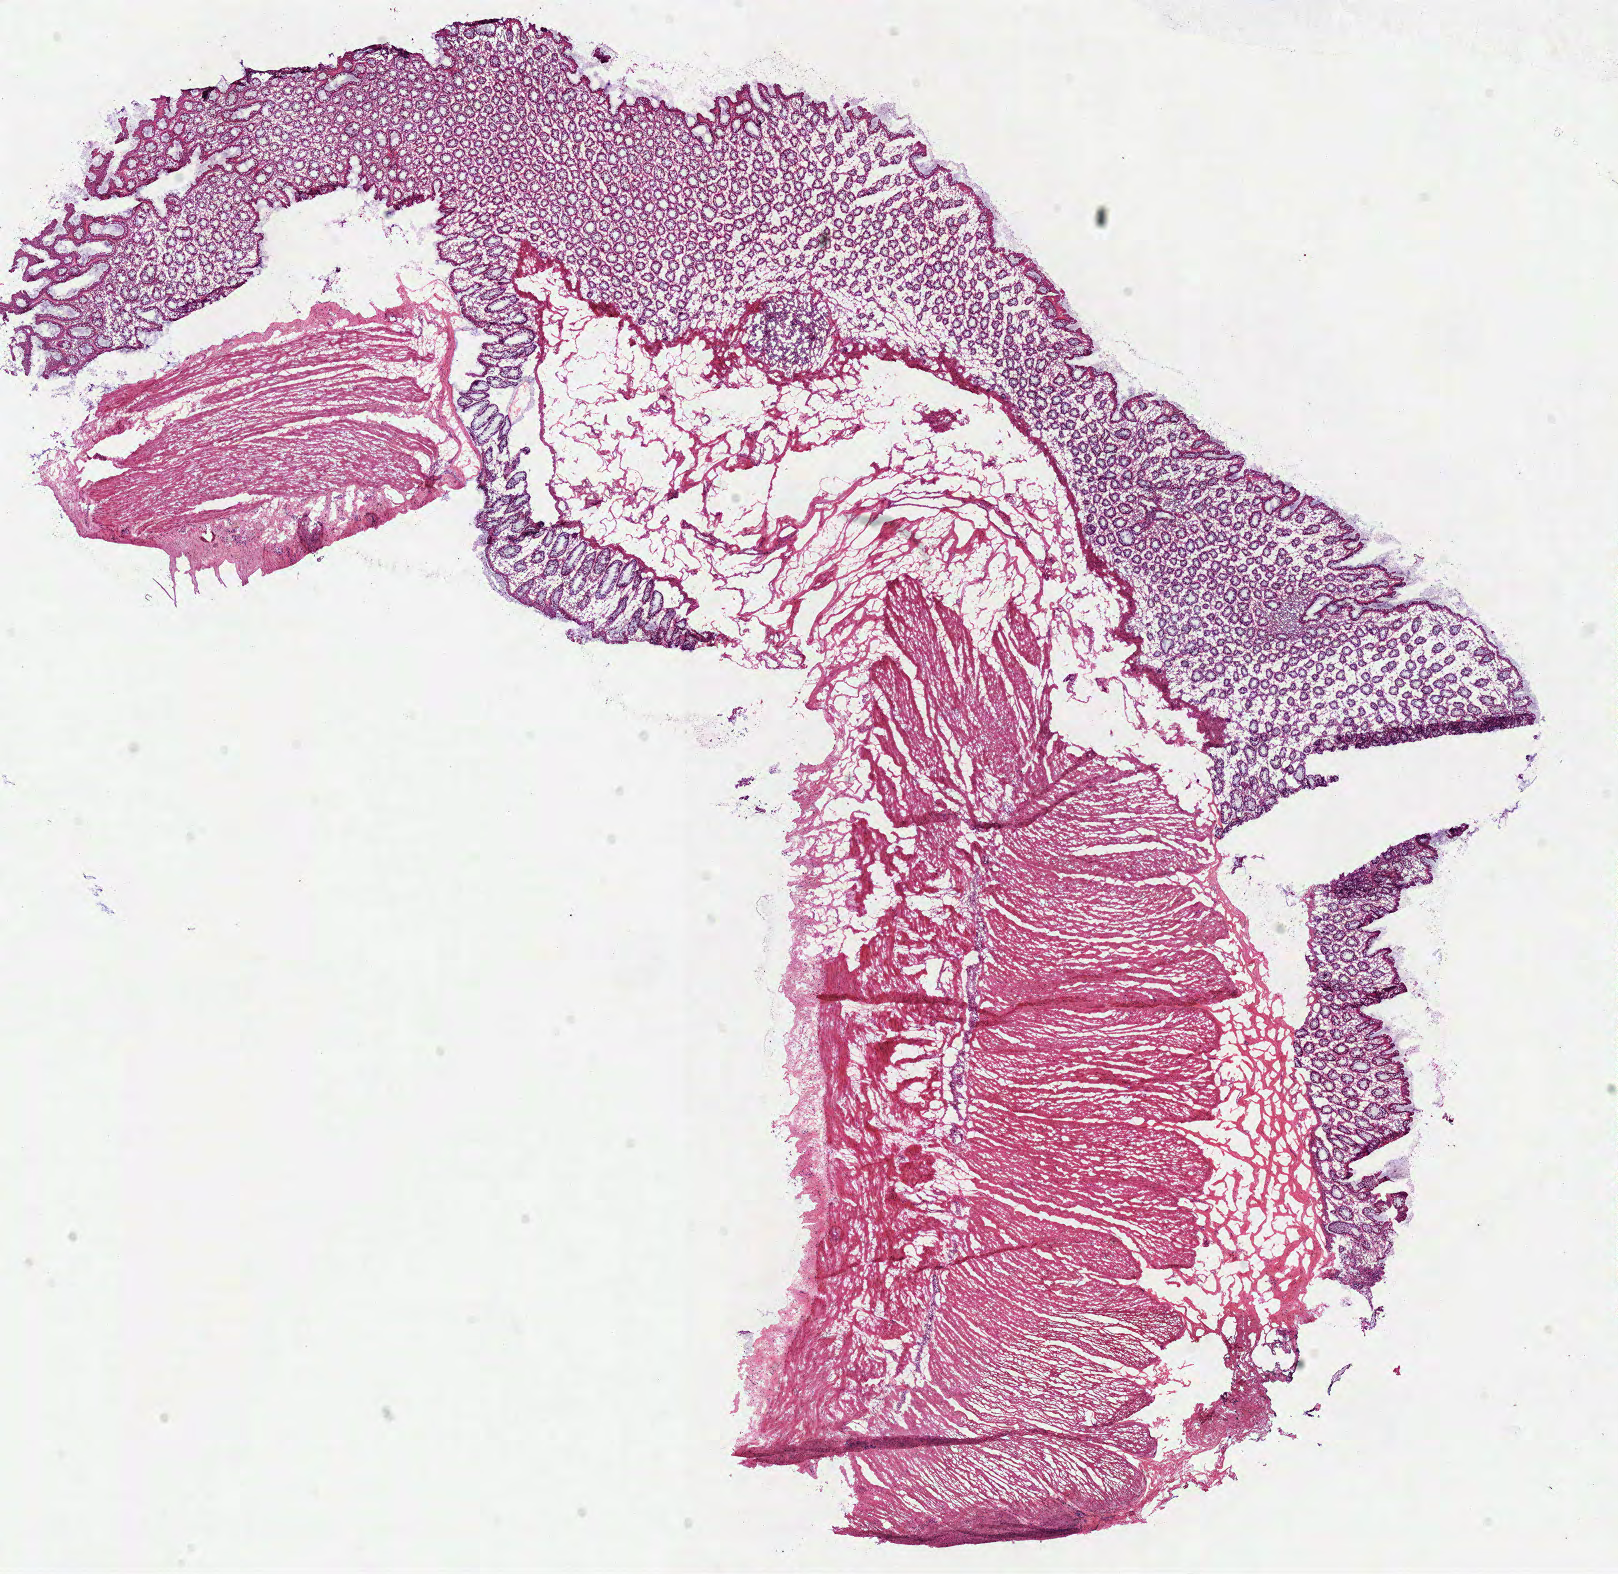
H&E-stained whole-slide image — low-resolution overview of the scanned area, about 12.7 x 12.4 mm (from a 40x scan), frozen section from the top of the tissue portion, sample: solid tissue normal (non-tumour tissue), colon. Female patient; age at initial diagnosis 55 years.
This section: solid tissue normal sample (biorepository sample class). Patient diagnosis: Adenocarcinoma, NOS (sigmoid colon).